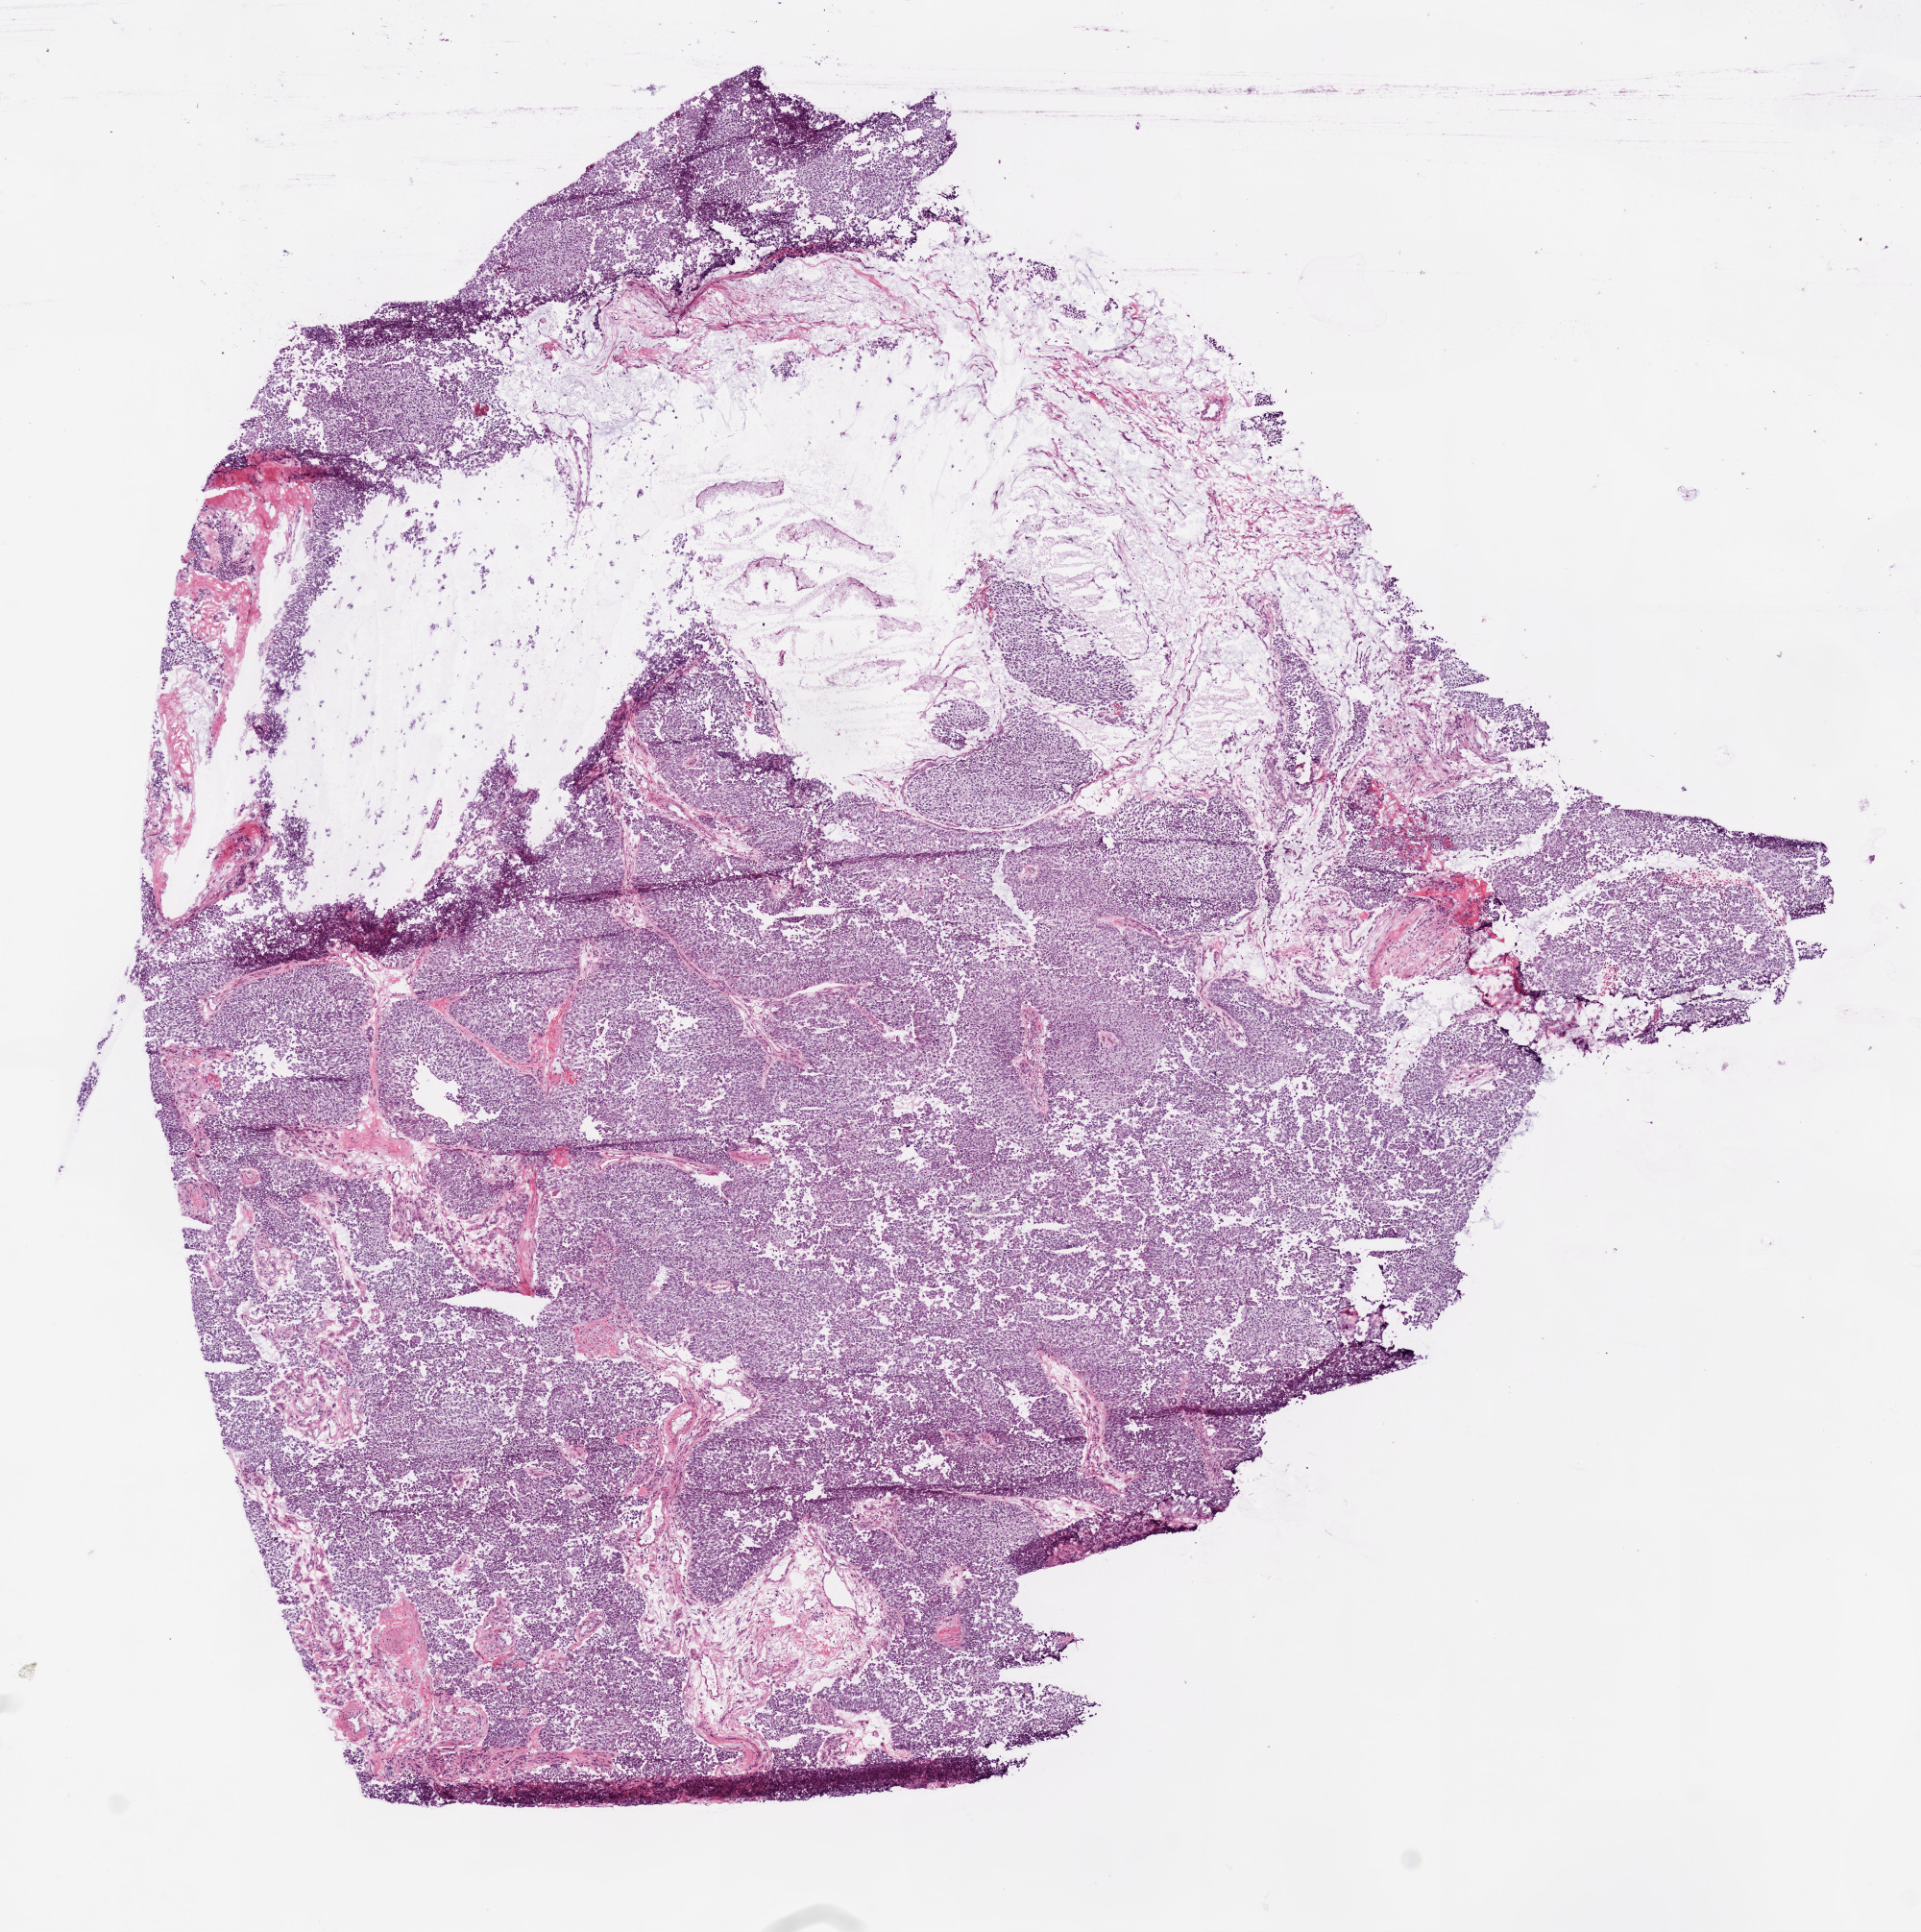
Digitized H&E tissue section (whole slide) — low-resolution overview of the scanned area, about 8.0 x 8.1 mm (acquisition: 20x scan). Frozen section from the top of the tissue portion. Kidney, primary tumour sample. Male patient; age at initial diagnosis 75 years. Composition of this section per pathologist review: tumour cells 90%, tumour nuclei 85%, normal cells 0%, stromal cells 5%, necrosis 5%.
Laterality: right. AJCC pathologic stage: II. TNM: T2 NX M0. Histologic diagnosis: Papillary adenocarcinoma, NOS.